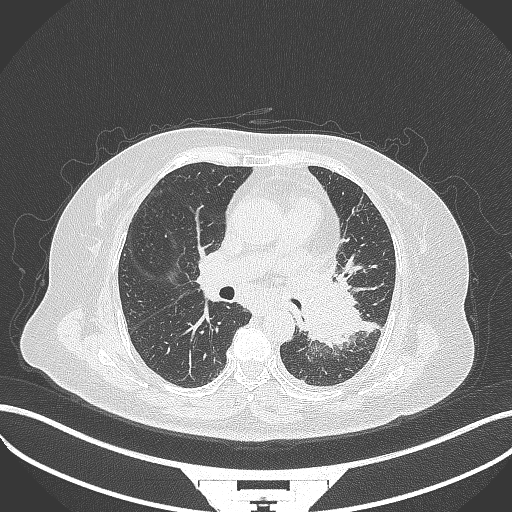
Chest CT, one axial slice. Position 191 of 322 along the scan axis. Reconstruction kernel B70f. 120 kVp. Lung window (W 1500 / L -600 HU). 1 mm slice thickness. 512 × 512 image matrix, field of view 400 × 400 mm. Female patient, age 69 years. Case-level facts recorded for this patient, not image findings: clinical TNM (as recorded): T2b N3 M1.
Structures marked on this image (bounding box drawn by a radiologist):
- lung tumour (recorded histology: adenocarcinoma): bounding box <295,275,361,346> (left, top, right, bottom; pixels)